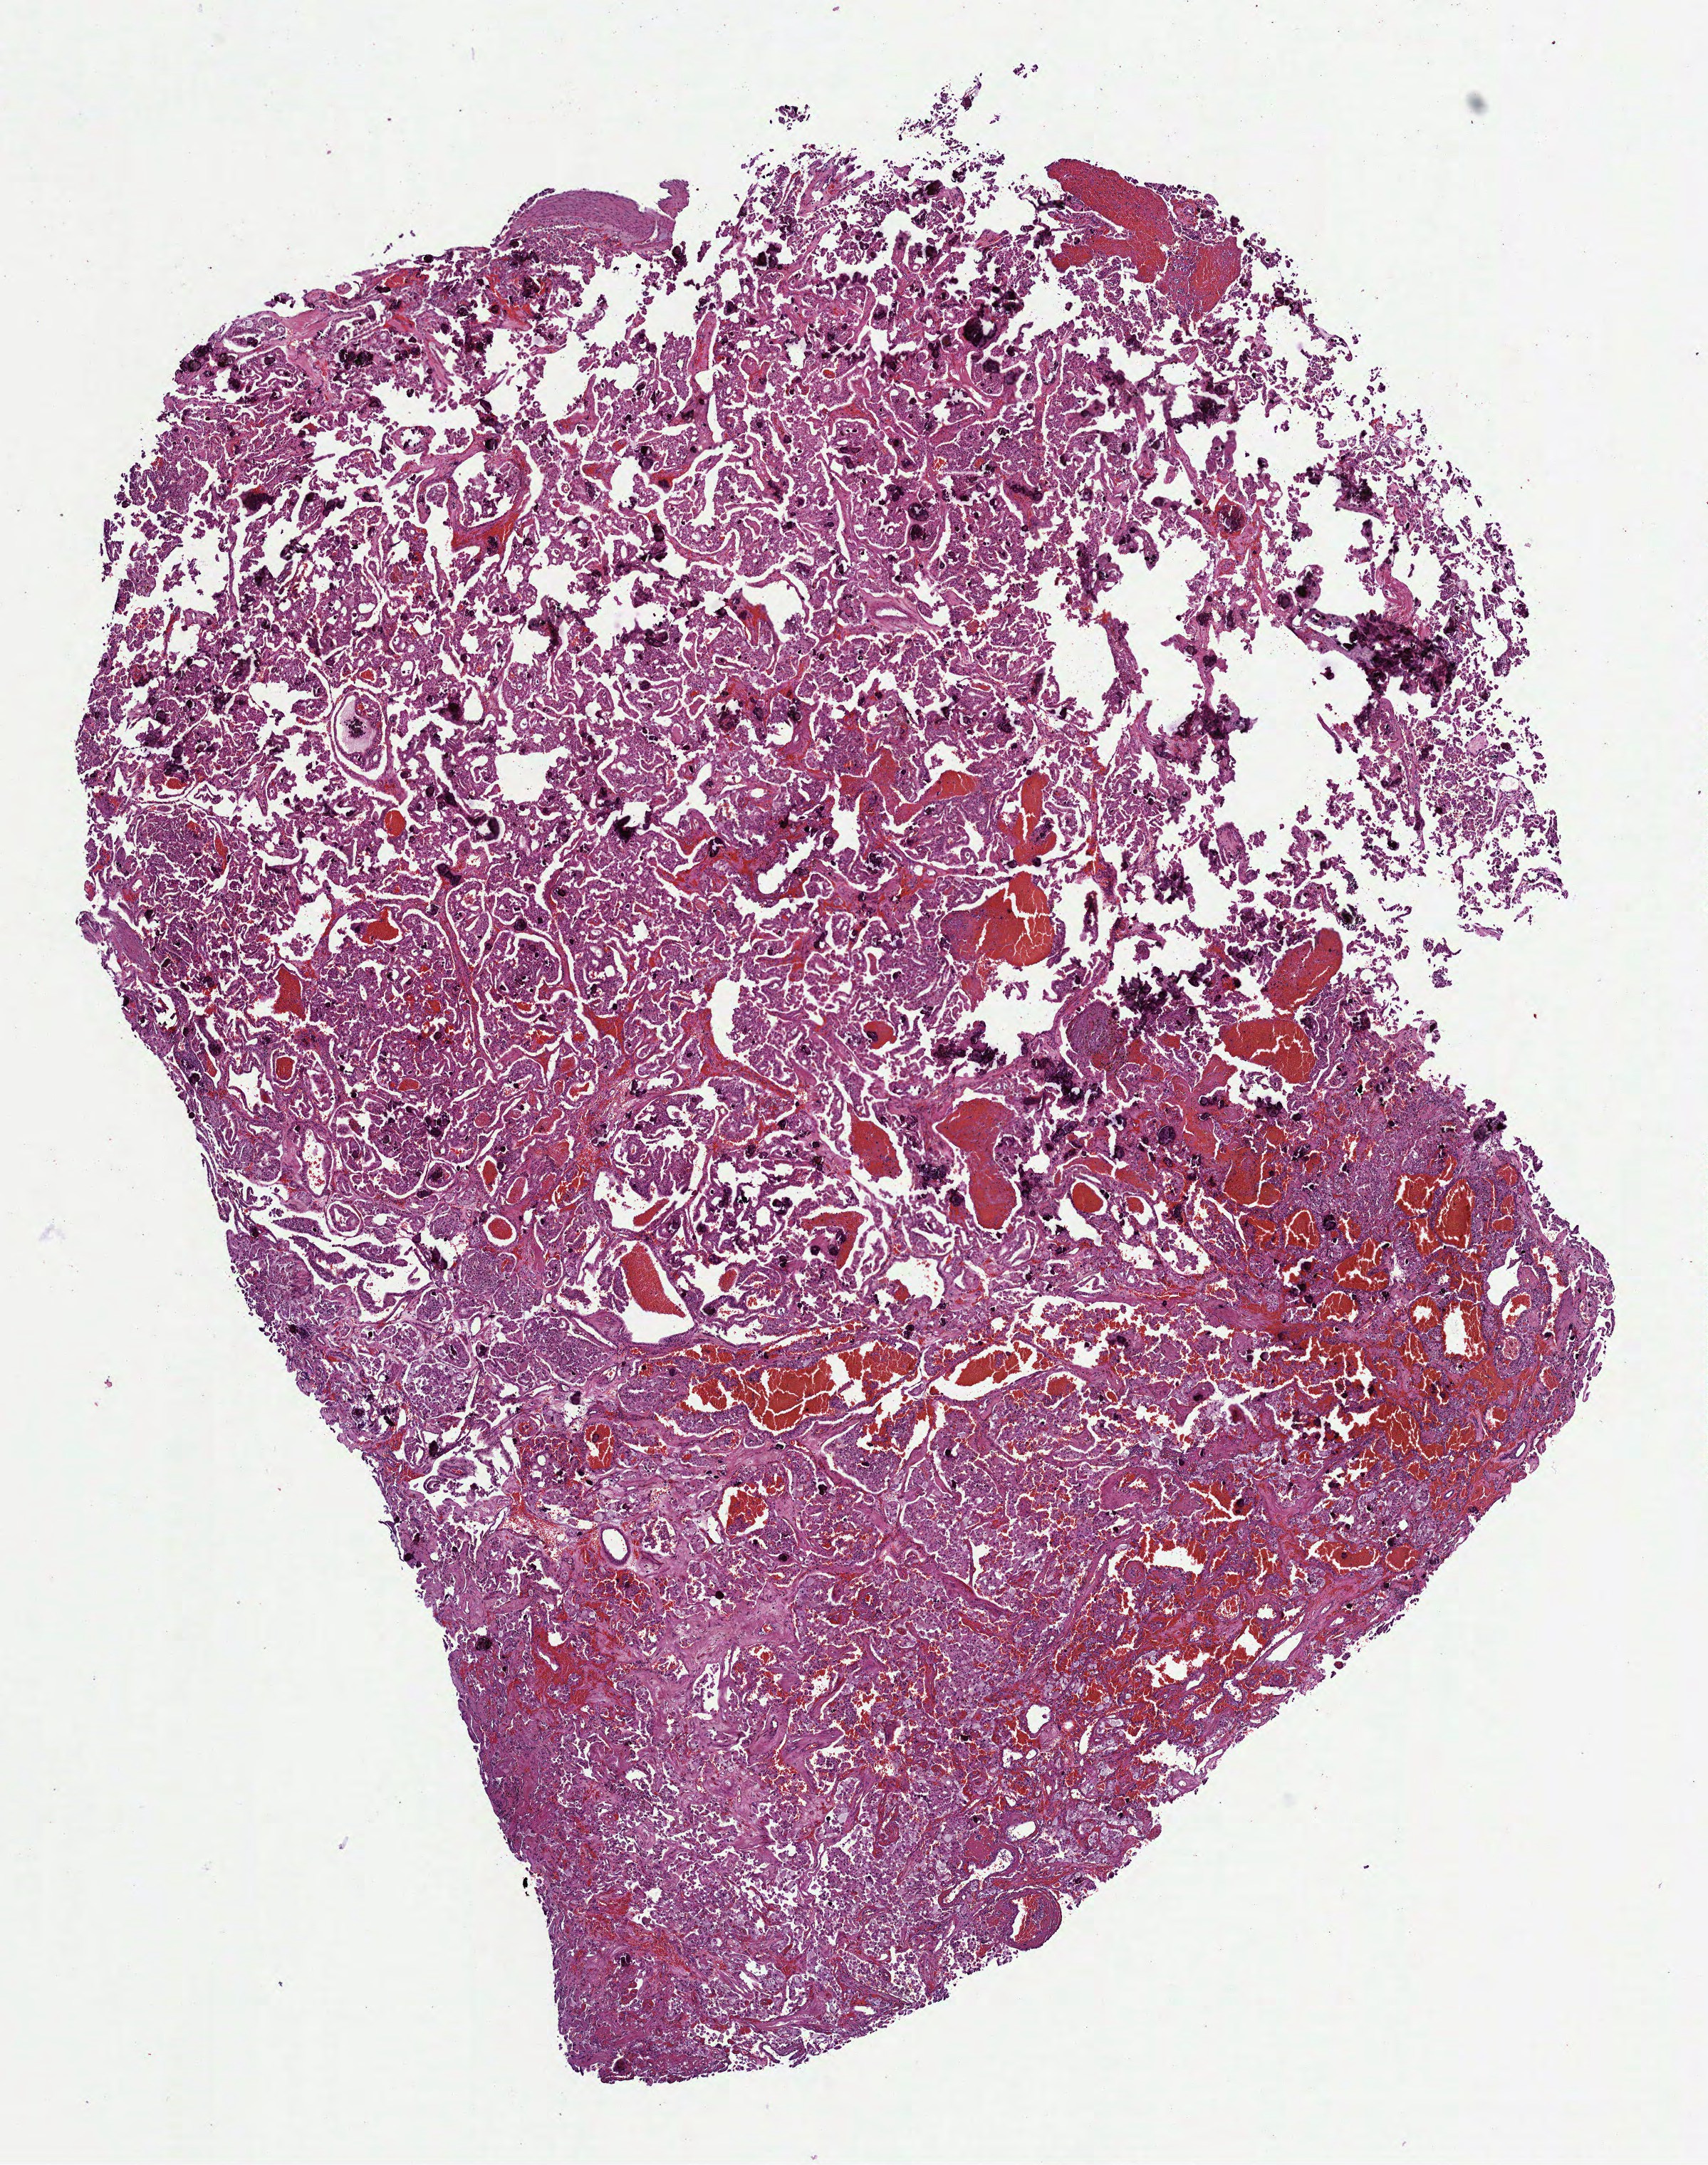
Whole-slide histology image, H&E, shown as a low-resolution overview of the whole scanned area (about 9.7 x 12.3 mm). Formalin-fixed paraffin-embedded (FFPE) diagnostic section. Sample: primary tumour, kidney. Patient: male, age at initial diagnosis 49 years.
* histologic diagnosis: Renal cell carcinoma, chromophobe type
* AJCC pathologic stage: II (7th edition)
* laterality: left